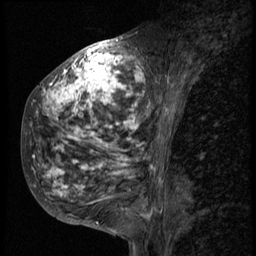
Breast MRI (dynamic contrast-enhanced), one sagittal slice. Slice 25 of 58 in the series (ordered by position). 3 images stored at this slice position (order not interpretable as contrast timing). 1.5 T. TE 4.2 ms, TR 9 ms. 256 × 256 image matrix, field of view 180 × 180 mm. Female patient, age 50 years. Case-level facts recorded for this patient, not image findings: setting: breast cancer imaged before/during neoadjuvant chemotherapy; receptor status: triple-negative.
Annotated regions visible in this slice (semi-automatic segmentation, software-assisted and operator-edited):
- analysis volume of interest (the breast-tissue region the enhancement analysis was run in; not a lesion): bounding box (x1, y1, x2, y2) in pixels: (23, 48, 165, 214)
- tumour enhancement mask (voxels above the 140 % enhancement threshold inside the analysis volume of interest): (31, 49, 163, 214)